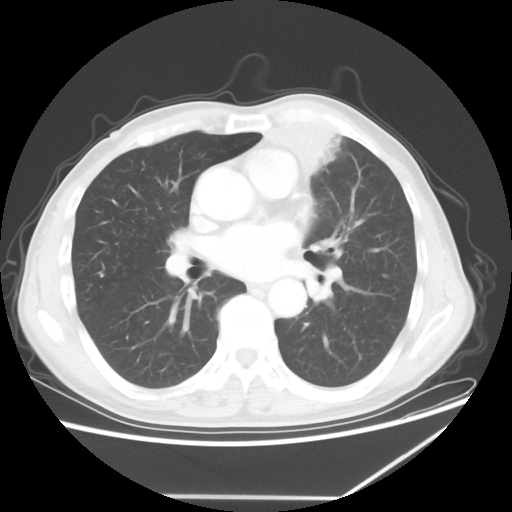
Chest CT, one axial slice; slice 32 of 64 in the series (ordered by position); reconstruction kernel STANDARD; 100 kVp; lung window (W 1500 / L -600 HU); 512 × 512 image matrix, field of view 383 × 383 mm. Male patient, age 64 years. Case-level facts recorded for this patient, not image findings: clinical TNM (as recorded): T1c N1 M1; histopathological grade: G2.
Outlined on this slice (bounding box drawn by a radiologist):
- lung tumour (recorded histology: squamous cell carcinoma): box from (x=261, y=117) to (x=338, y=198) px